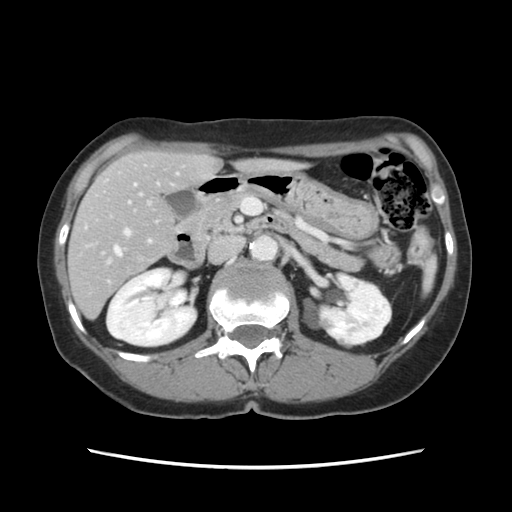
Contrast-enhanced abdominal CT, one axial slice; slice 58 of 120 in the series (ordered by position); 120 kVp; intravenous contrast given; soft-tissue window (W 400 / L 40 HU); 512 × 512 image matrix. Female patient, age 70 years. From the clinical record (not read from this slice): diagnosis: colorectal cancer liver metastases, imaged before liver resection; multiple liver metastases: no; largest metastasis: 2.5 cm; disease in both lobes: no.
Annotated regions visible in this slice (outlined manually by an expert reader):
- hepatic veins: bounding box [x1, y1, x2, y2] px = [114, 247, 121, 256]
- liver: [69, 152, 288, 316]
- planned liver remnant (the part of the liver to remain after resection): [71, 151, 287, 297]
- portal vein (with intrahepatic branches): [124, 174, 178, 243]